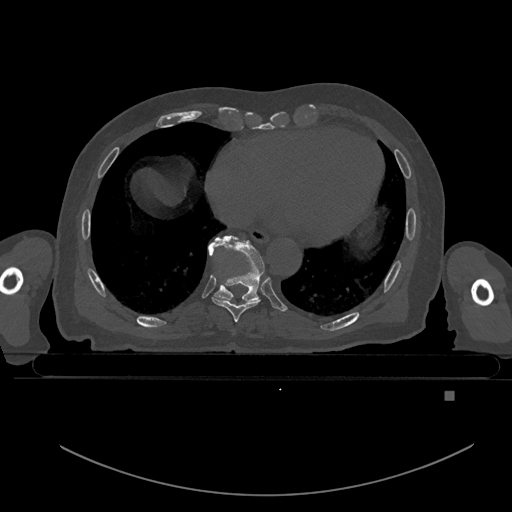
CT including the spine, one axial slice; bone window (W 1800 / L 400 HU); 512 × 512 image matrix, field of view 456 × 456 mm. Patient: male, 82 years. From the clinical record (not read from this slice): primary cancer: prostate; vertebrae with lytic lesions (as recorded): T11, T9, T8, T2.
Outlined on this slice (semi-automatic segmentation, software-assisted and operator-edited):
- T8 vertebra: bounding box <212,296,261,322> (left, top, right, bottom; pixels)
- T9 vertebra: <208,235,265,303>